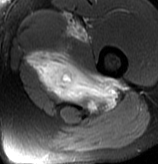
MRI of an extremity soft-tissue mass, one axial slice; slice 65 of 70 in the series (ordered by position); T2-weighted fat-saturated; MR volume resampled by the dataset authors to the PET/CT grid (not the native acquisition matrix); 158 × 164 image matrix, field of view 154 × 160 mm. Male patient. Case-level facts recorded for this patient, not image findings: histological type: extraskeletal osteosarcoma; grade: high; site of the primary tumour: left adductur.
Annotated regions visible in this slice (expert contour drawn on MRI and transferred to this co-registered scan by the dataset authors):
- gross tumour volume (mass): box from (x=26, y=14) to (x=128, y=113) px